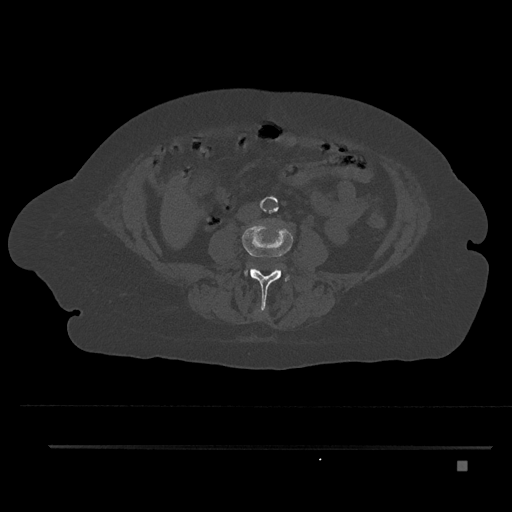
CT including the spine, one axial slice; slice 118 of 797 in the series (ordered by position); bone window (W 1800 / L 400 HU); 0.5 mm slice thickness; 512 × 512 image matrix, field of view 437 × 437 mm. Female patient, age 76 years. Case-level facts recorded for this patient, not image findings: primary cancer: lung; vertebrae with lytic lesions (as recorded): T11, L3.
Annotated regions visible in this slice (semi-automatically segmented with operator editing):
- L2 vertebra: bounding box (x1, y1, x2, y2) in pixels: (256, 308, 264, 315)
- L3 vertebra: (242, 219, 293, 309)
- L4 vertebra: (248, 263, 289, 281)